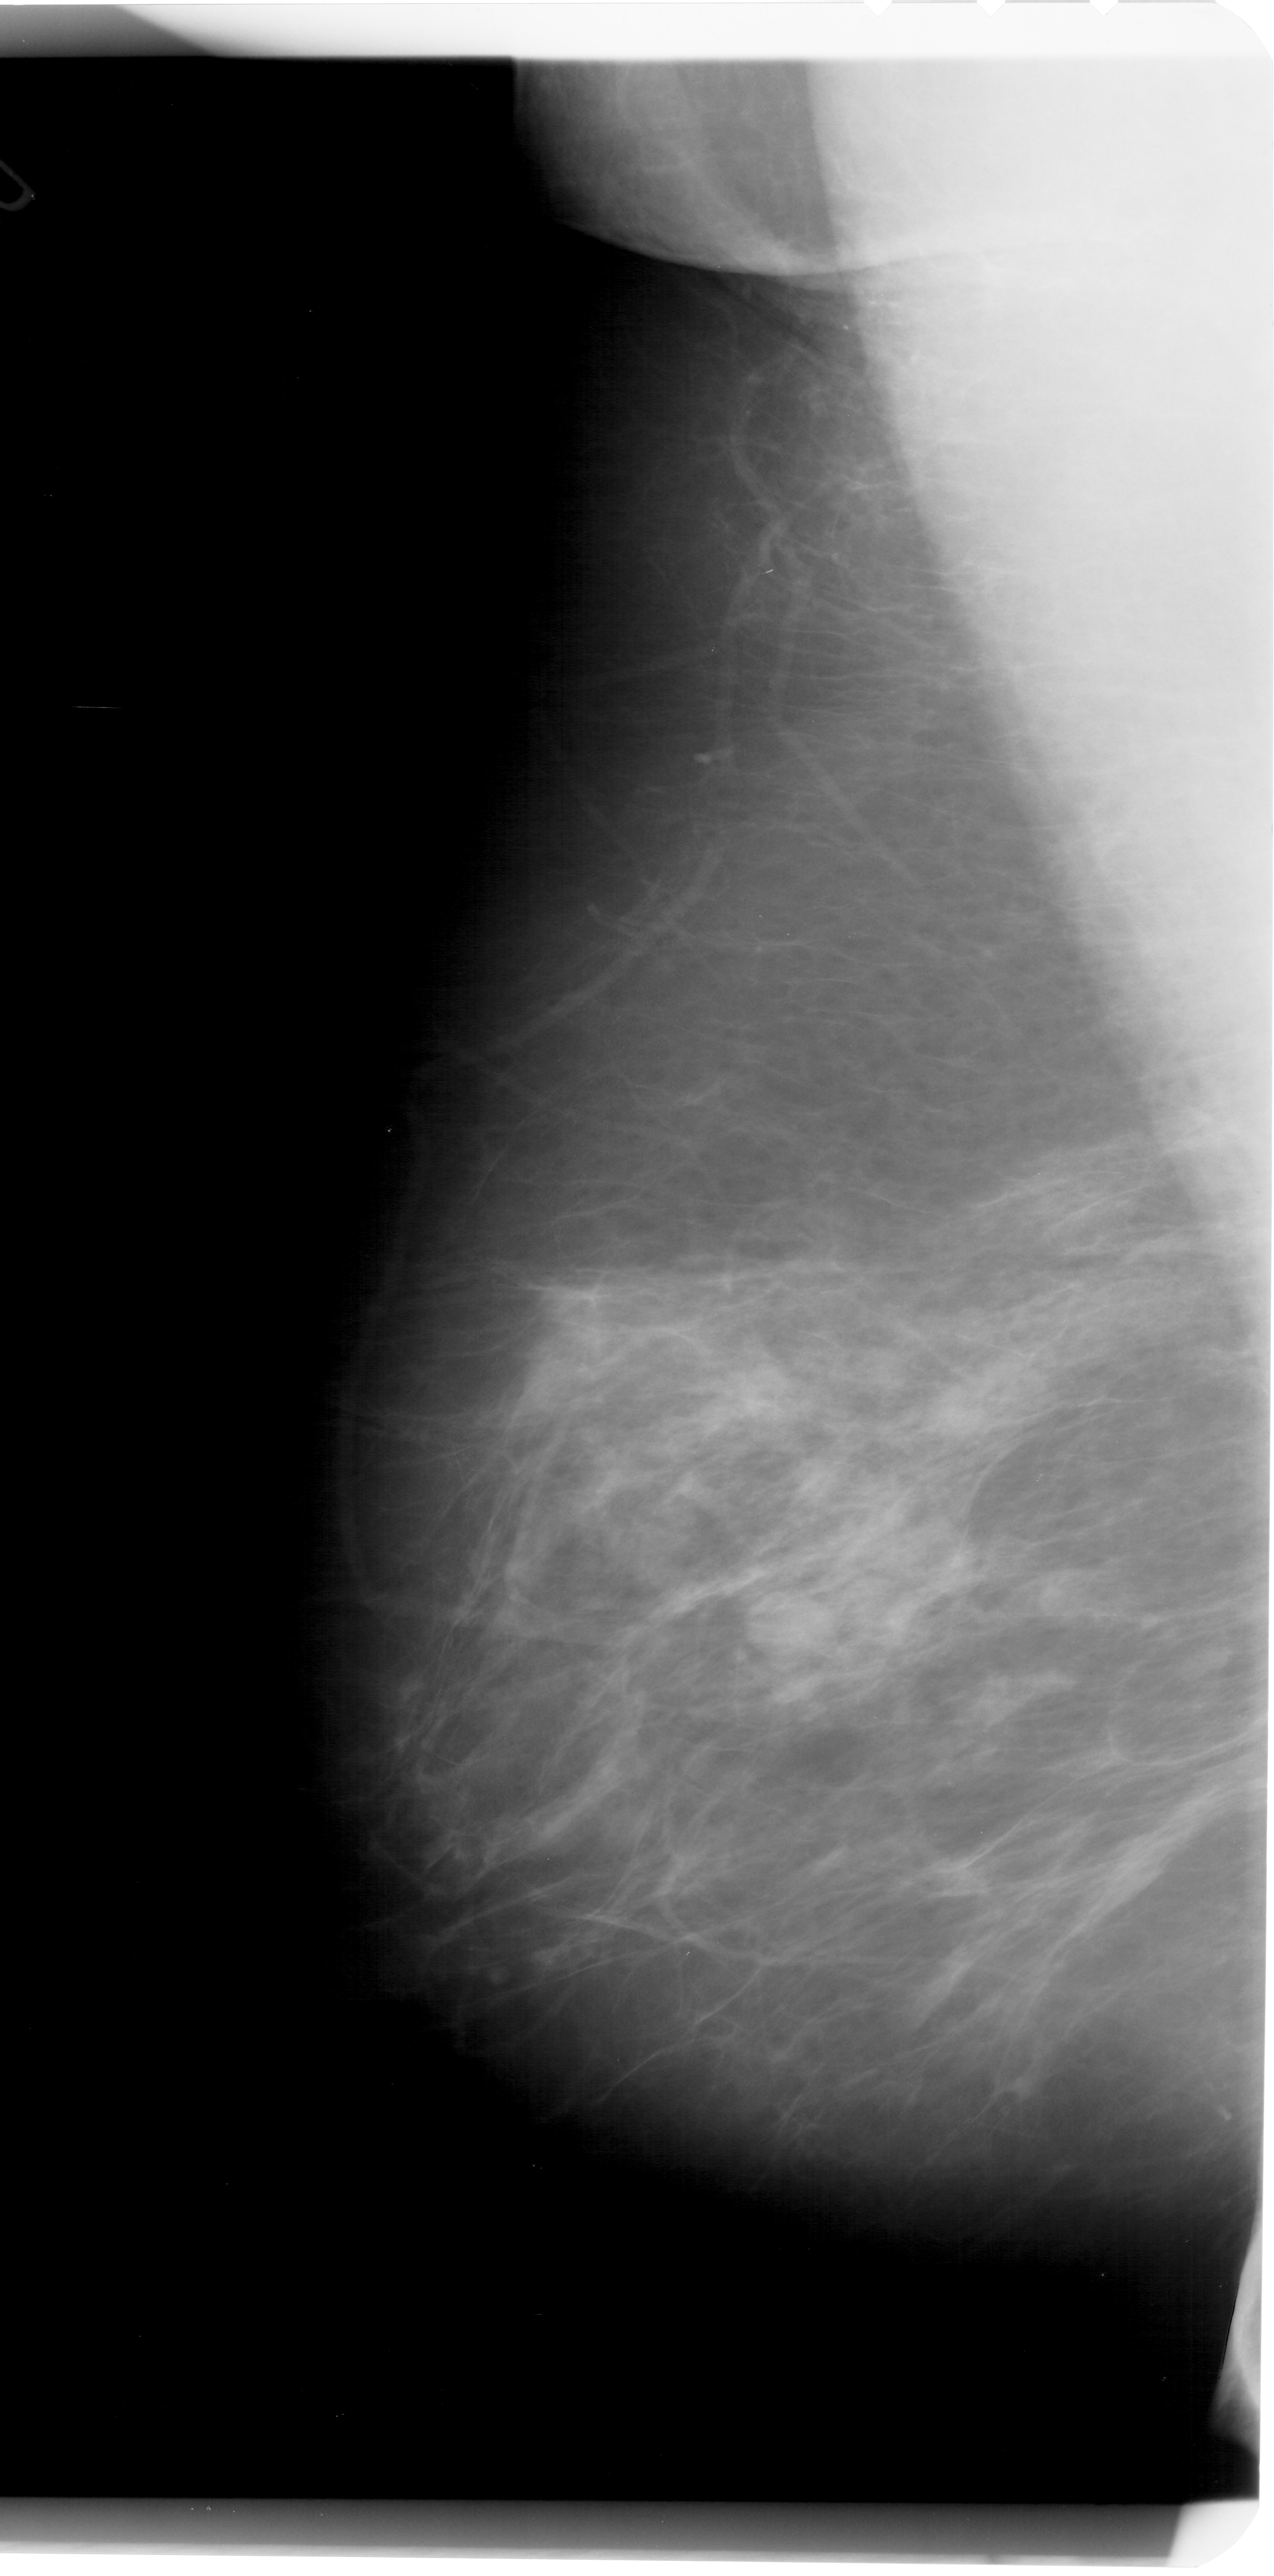
Mammogram (digitized film). Left breast. MLO view. Breast composition: scattered fibroglandular densities (BI-RADS density category 2 of 4). 1274 × 2576 image matrix.
Marked abnormalities (boxes around the expert regions of interest):
- mass, shape oval, margins obscured; BI-RADS assessment category 3; subtlety rating 3 on a 1 (subtle) to 5 (obvious) scale; pathology result (as recorded, not read from the image): benign: box from (x=752, y=1582) to (x=842, y=1660) px